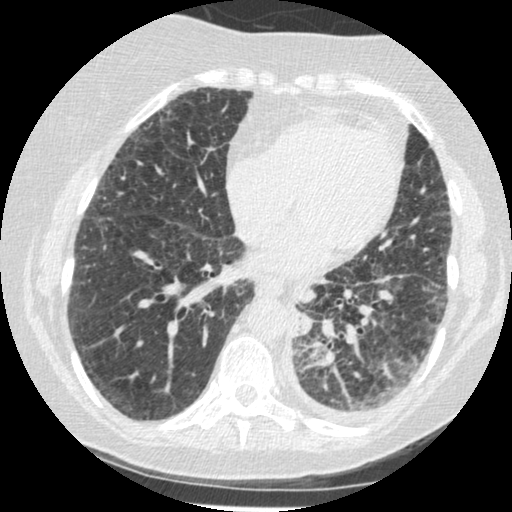
Low-dose screening chest CT, one axial slice; slice 74 of 341 in the series (ordered by position); lung window (W 1500 / L -600 HU); 1.25 mm slice thickness; 512 × 512 image matrix, field of view 310 × 310 mm.
Outlined on this slice (expert manual segmentation):
- lesion 1 (tumor, lower lobe of left lung): bounding box [x1, y1, x2, y2] px = [294, 324, 310, 335]